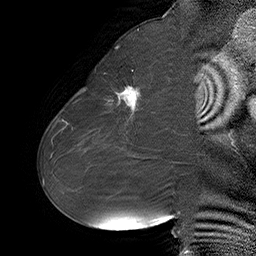
Breast MRI (dynamic contrast-enhanced), one sagittal slice. Position 27 of 55 along the scan axis. Dynamic contrast-enhanced series, time point 2 of 6 at this slice position (early post-contrast). 1.5 T. TE 4.5 ms, TR 32.4 ms. 3 mm slice thickness. 256 × 256 image matrix, field of view 180 × 180 mm. Female patient. From the clinical record (not read from this slice): setting: breast cancer imaged before/during neoadjuvant chemotherapy; receptor status: HER2-positive.
Structures marked on this image (semi-automatic segmentation, software-assisted and operator-edited):
- analysis volume of interest (the breast-tissue region the enhancement analysis was run in; not a lesion): bounding box <80,64,163,134> (left, top, right, bottom; pixels)
- tumour enhancement mask (voxels above the 100 % enhancement threshold inside the analysis volume of interest): <115,86,139,113>